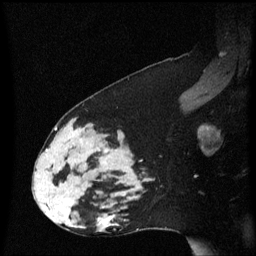
Breast MRI (dynamic contrast-enhanced), one sagittal slice. Position 38 of 60 along the scan axis. Dynamic contrast-enhanced series, image 2 of 3 at this slice position (ordered by acquisition). 1.5 T. TE 4.2 ms, TR 8.4 ms. 2 mm slice thickness. 256 × 256 image matrix, field of view 210 × 210 mm. Patient: female, 33 years. From the clinical record (not read from this slice): setting: breast cancer imaged before/during neoadjuvant chemotherapy; receptor status: triple-negative.
Outlined on this slice (semi-automatically segmented with operator editing):
- analysis volume of interest (the breast-tissue region the enhancement analysis was run in; not a lesion): bounding box <44,123,139,189> (left, top, right, bottom; pixels)
- tumour enhancement mask (voxels above the 70 % enhancement threshold inside the analysis volume of interest): <106,149,110,154>